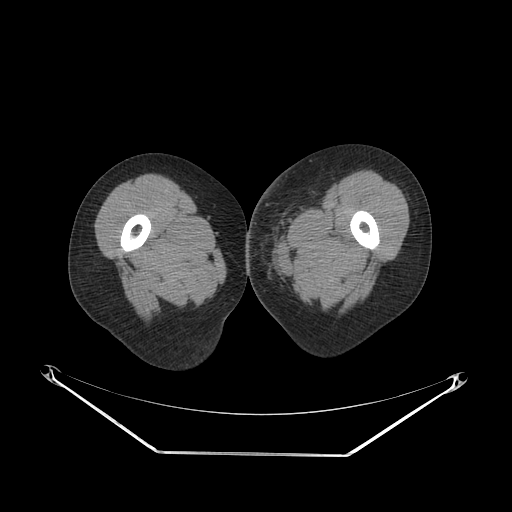
CT of an extremity soft-tissue mass (from a PET/CT study), one axial slice; slice 39 of 267 in the series (ordered by position); soft-tissue window (W 400 / L 40 HU); 3.75 mm slice thickness; 512 × 512 image matrix, field of view 500 × 500 mm. Female patient. From the clinical record (not read from this slice): histological type: leiomyosarcoma; grade: high; site of the primary tumour: groin.
Structures marked on this image (expert contour drawn on MRI and transferred to this co-registered scan by the dataset authors):
- gross tumour volume including surrounding oedema: bounding box [x1, y1, x2, y2] px = [244, 199, 302, 250]